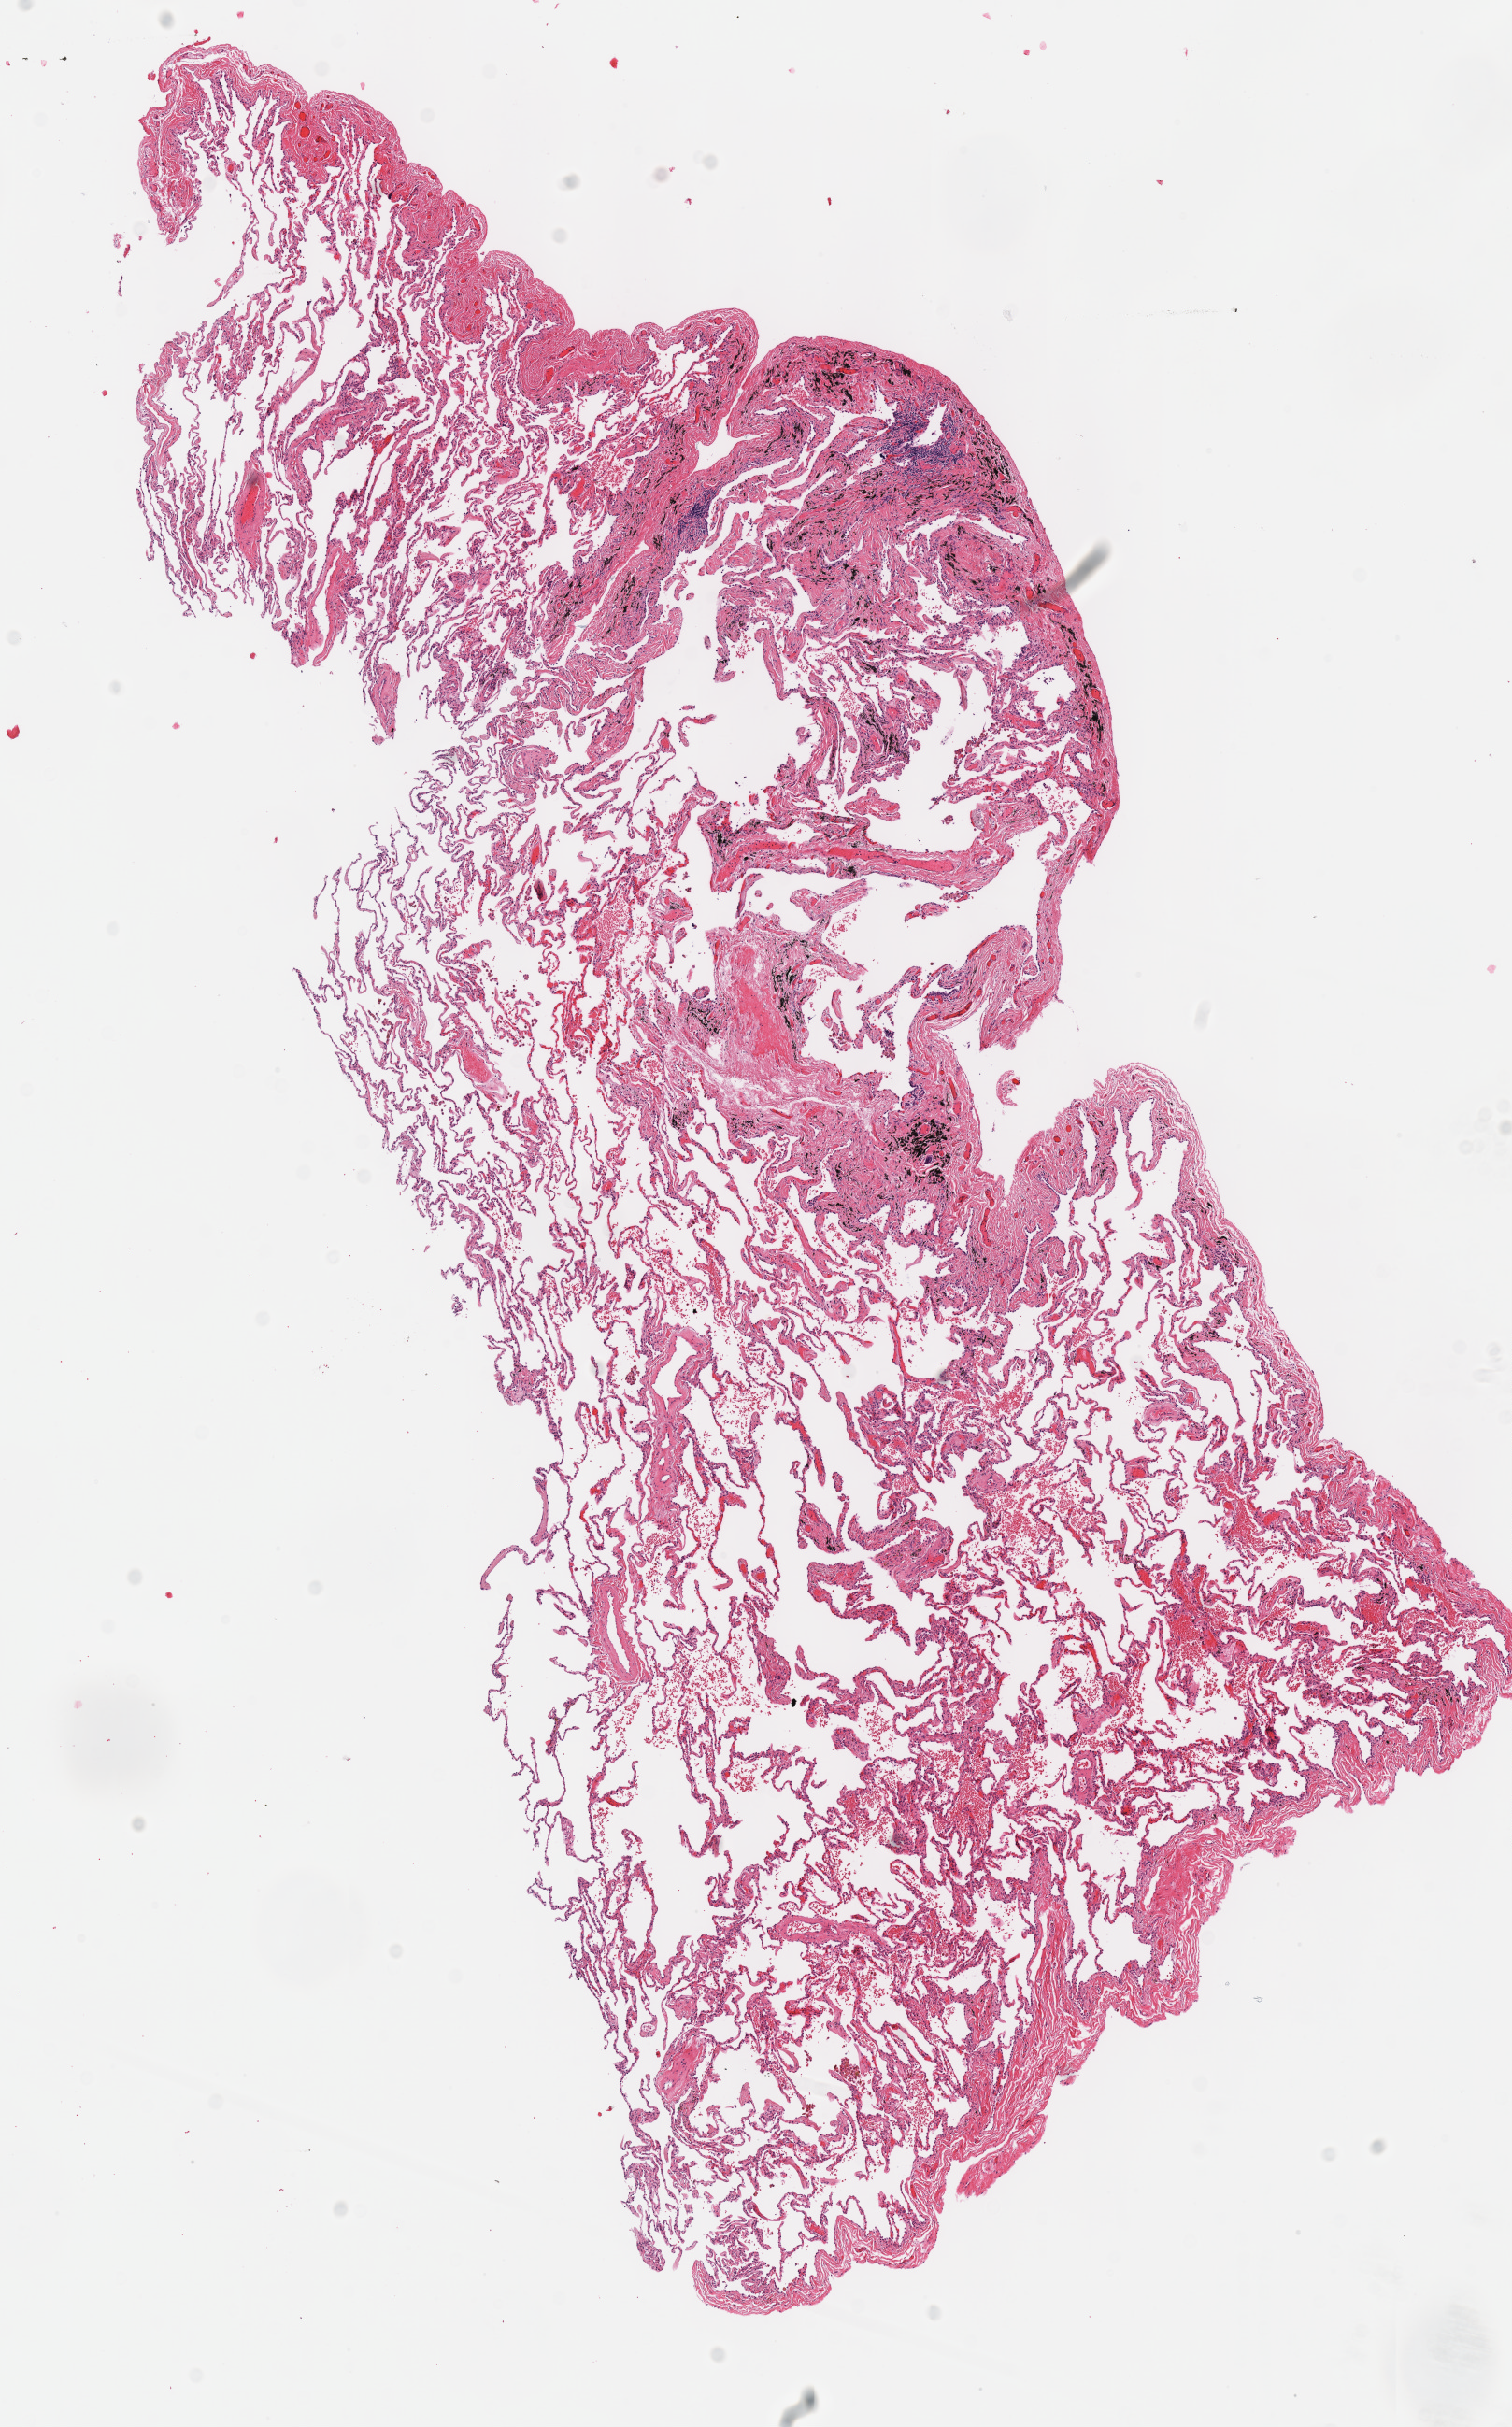
H&E whole-slide image, whole scanned area (about 6.4 x 10.2 mm, slide scanned at 40x) shown as a low-resolution overview; frozen section from the top of the tissue portion; lung, solid tissue normal (non-tumour tissue) sample. Male patient; age at initial diagnosis 61 years.
• this section: solid tissue normal (non-tumour) sample from the same patient
• patient diagnosis: Squamous cell carcinoma, NOS (upper lobe, lung)